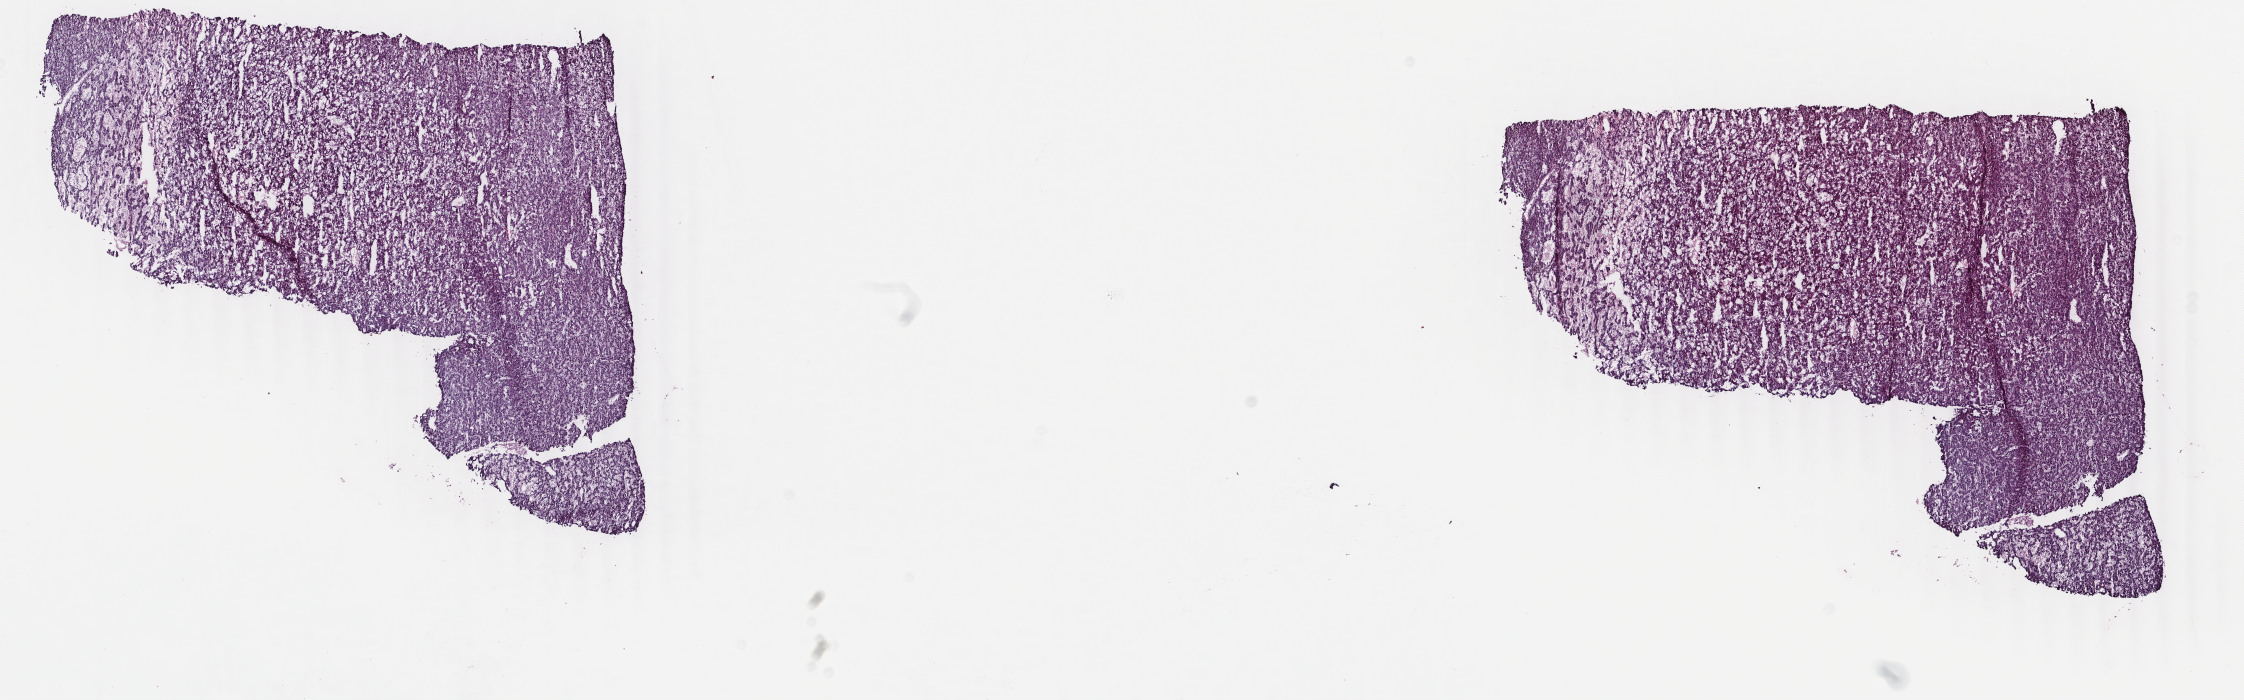
Whole-slide histology image, Hematoxylin and eosin (H&E) stained — a low-resolution overview of the entire scanned area, about 17.8 x 5.6 mm (acquisition: 40x scan); frozen section from the top of the tissue portion; primary tumour sample from the liver. Male patient; age at initial diagnosis 81 years. Histologic grade: G1 (well differentiated). Composition of this section per pathologist review: tumour cells 100%, tumour nuclei 95%, normal cells 0%, stromal cells 0%, necrosis 0%. Infiltration values recorded for this section: lymphocyte infiltration 0%, monocyte infiltration 0%, neutrophil infiltration 0%.
Histologic diagnosis: Hepatocellular carcinoma, NOS.